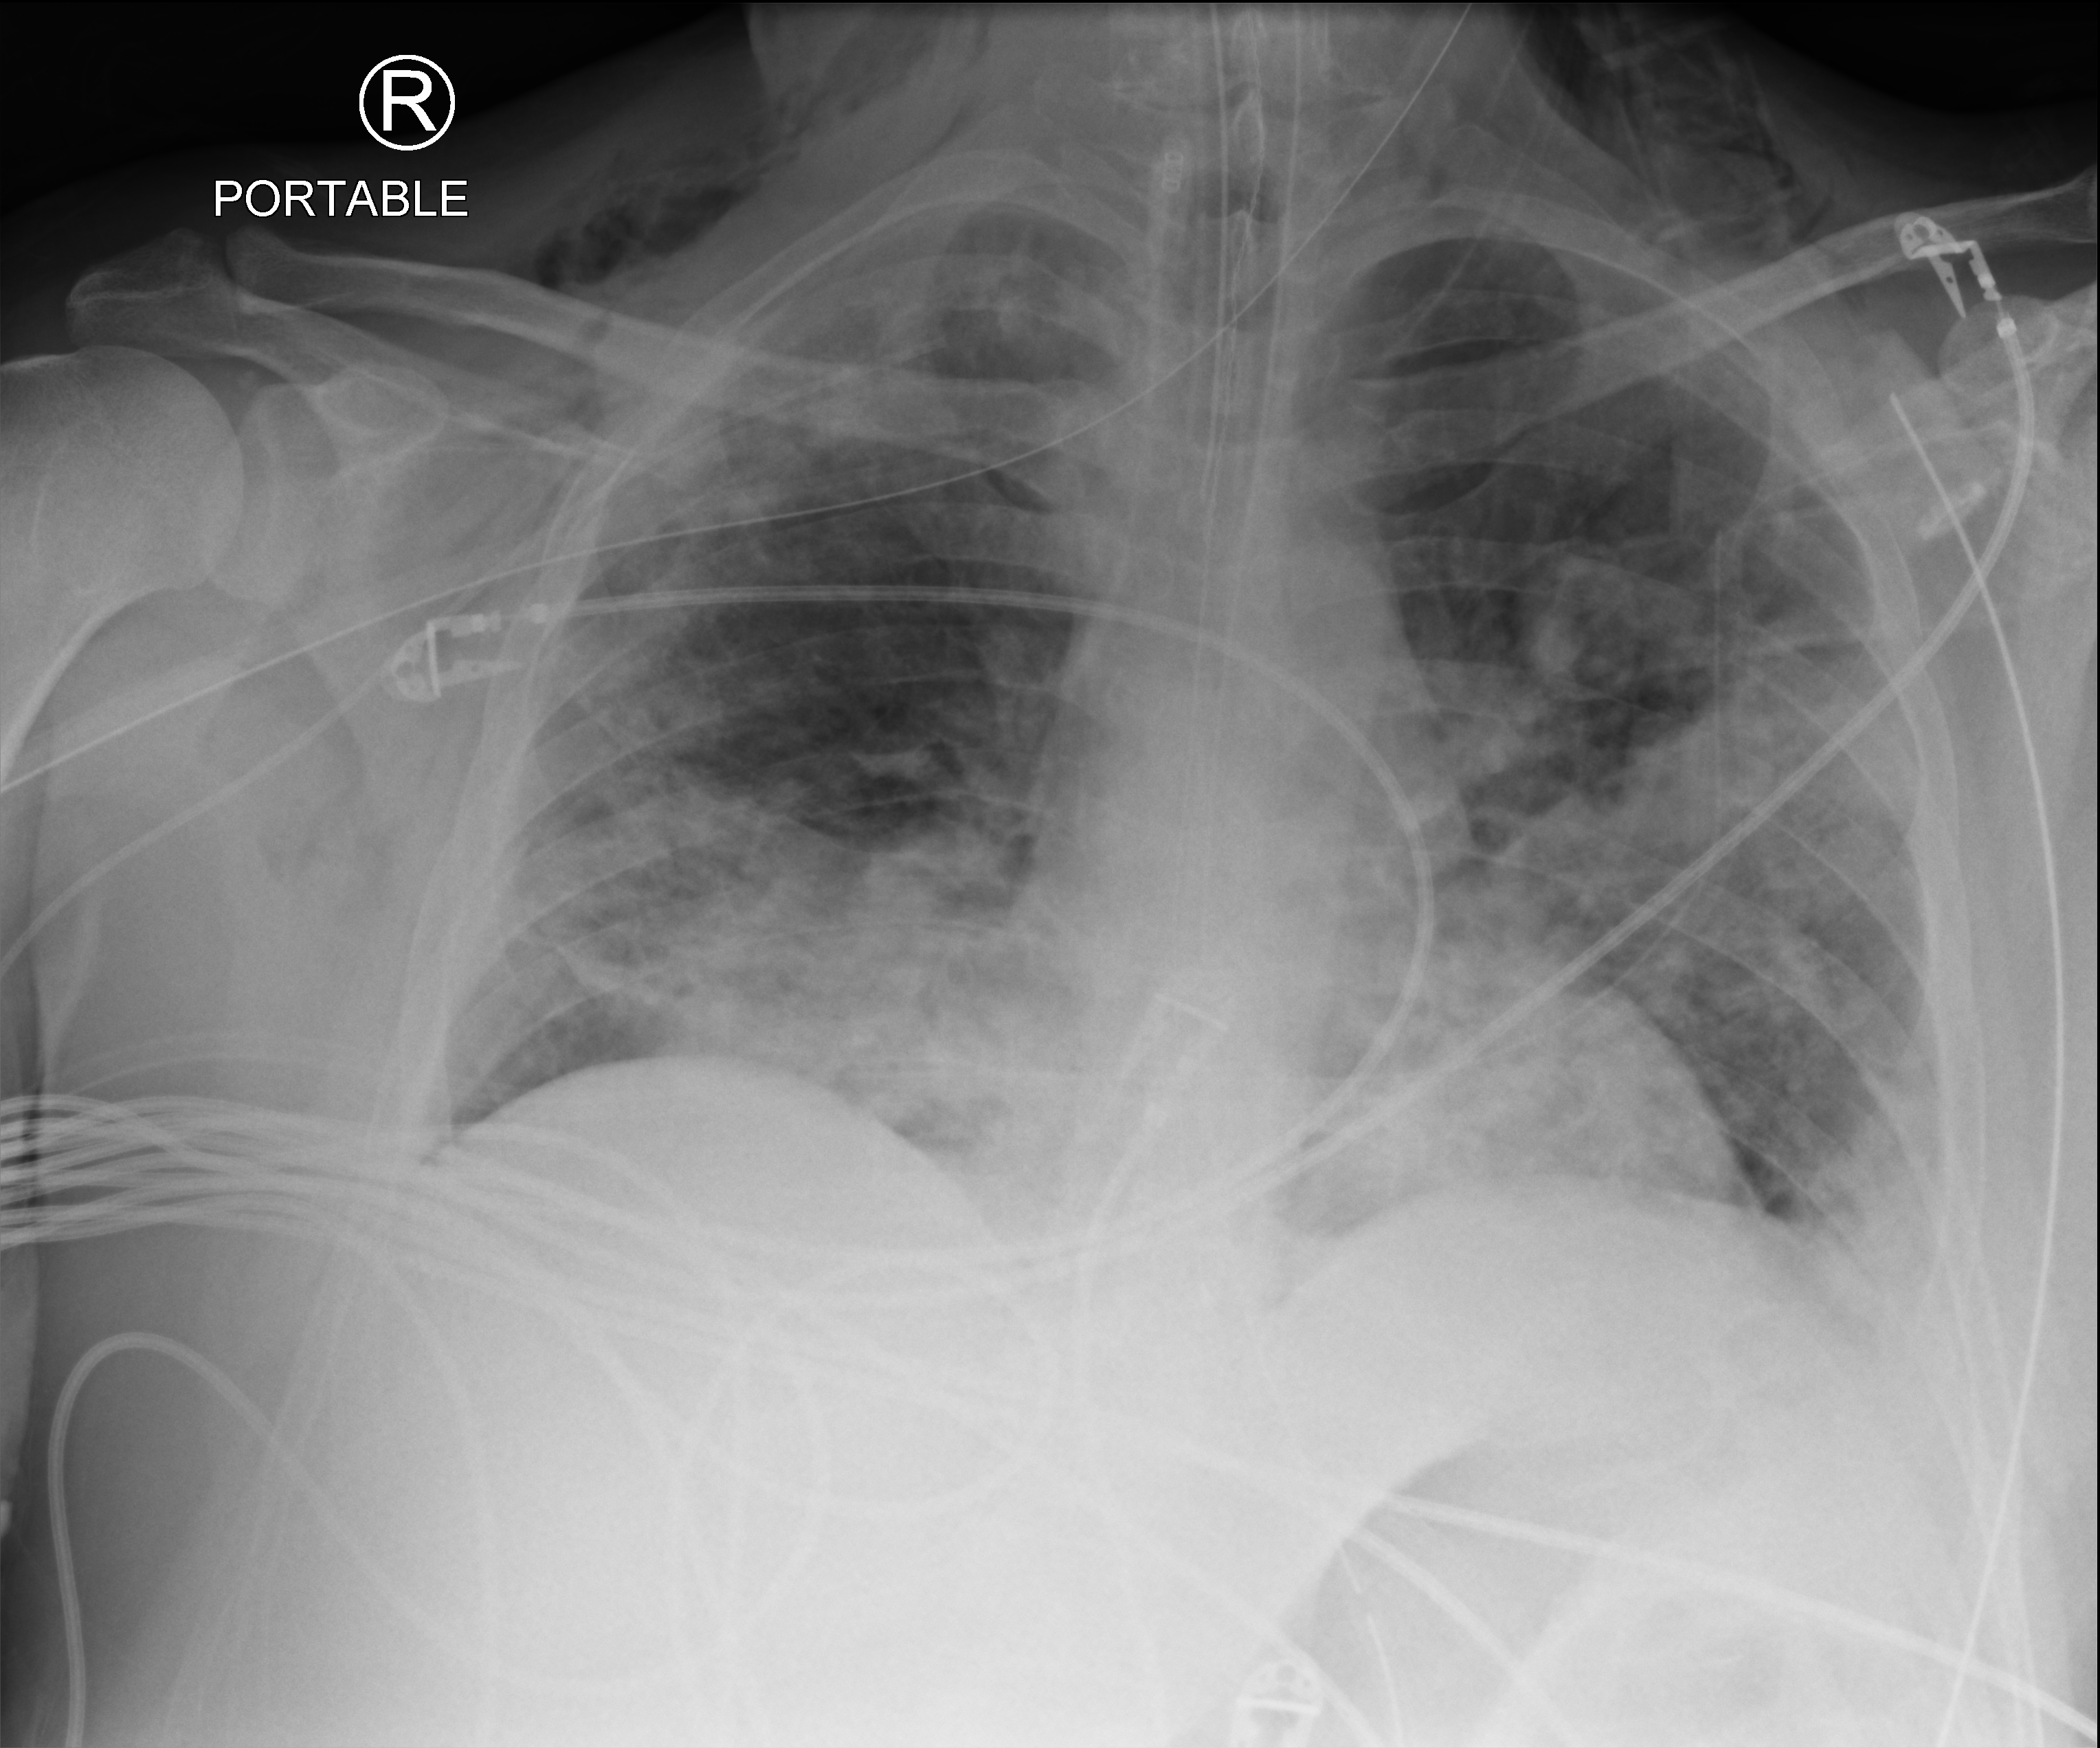
Chest X-ray (portable), anteroposterior (AP) projection. Patient hospitalised with COVID-19, aged 18–59 years.
From the hospital-stay record, not from the radiograph (when in the stay this image was taken is not recorded):
- other chronic lung disease (admission record): yes
- mechanically ventilated during this hospital stay: yes